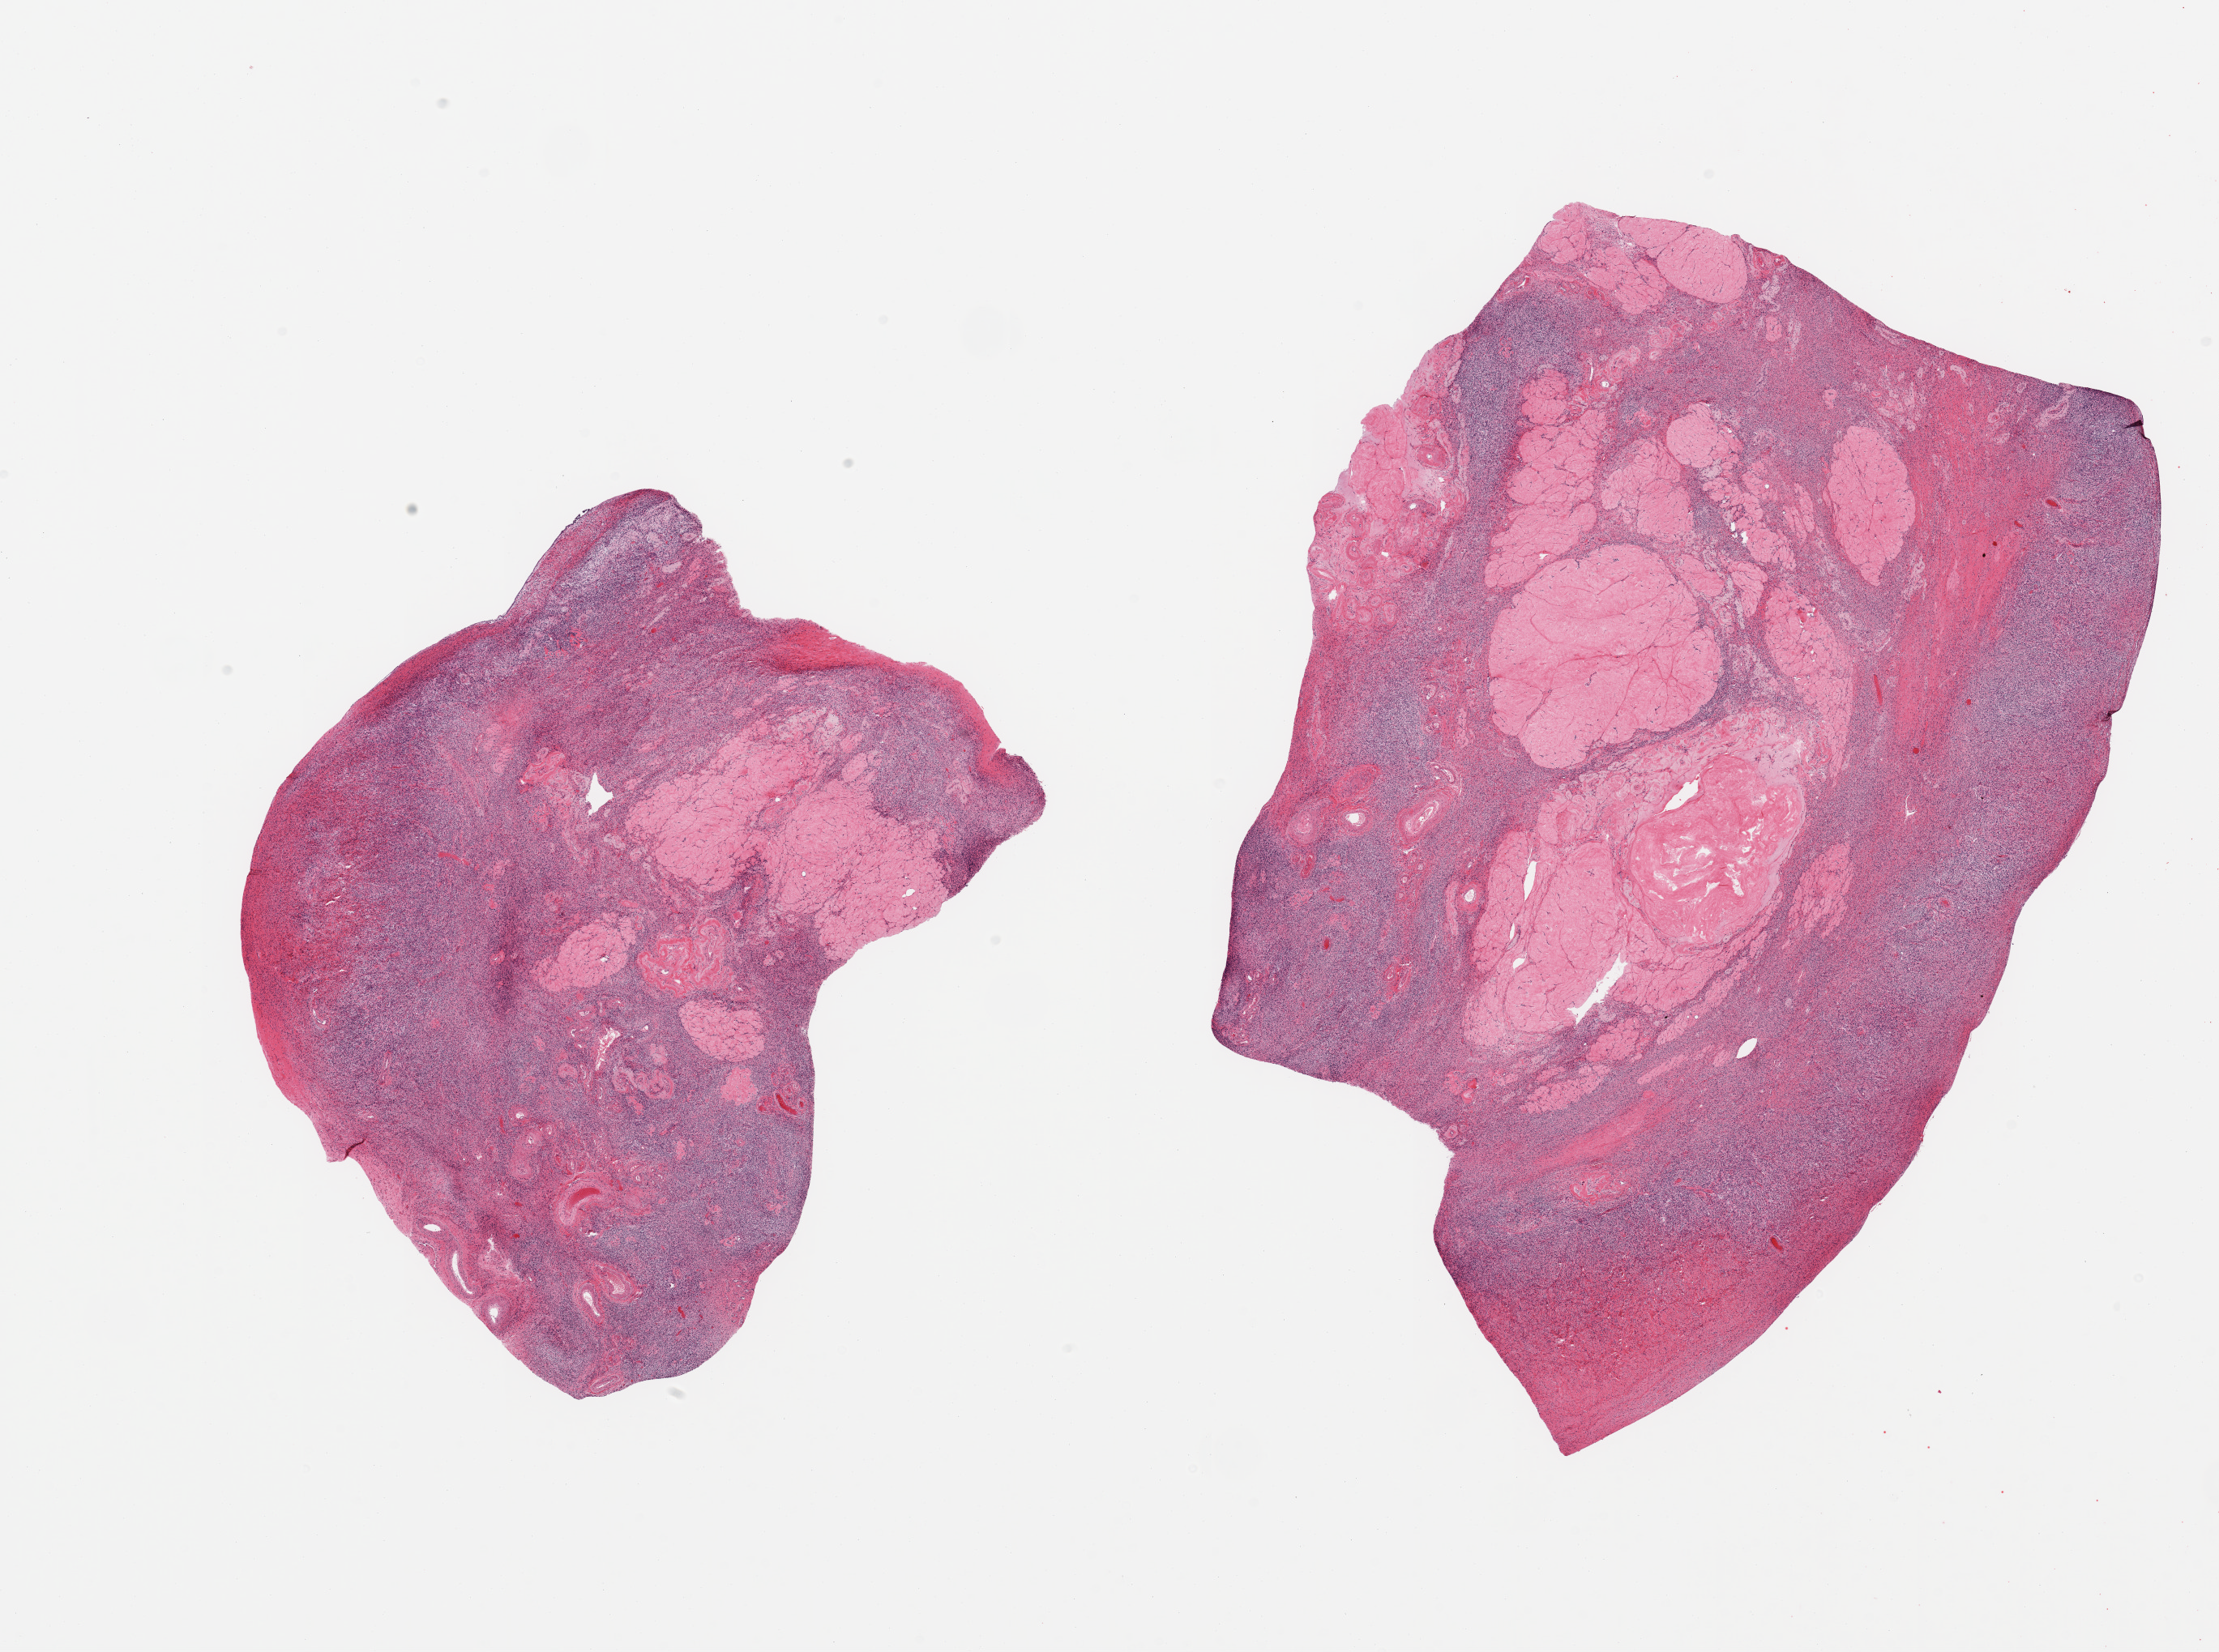
Whole-slide image, haematoxylin and eosin stain, brightfield — a low-resolution overview of the entire scanned area, about 21.7 x 16.1 mm, PAXgene-fixed paraffin-embedded (PFPE) section, section of ovary (target tissue), tissue donor sample. Donor sex: female.
- reviewer comment on this tissue sample: 2 pieces, post menopausal involutional changes